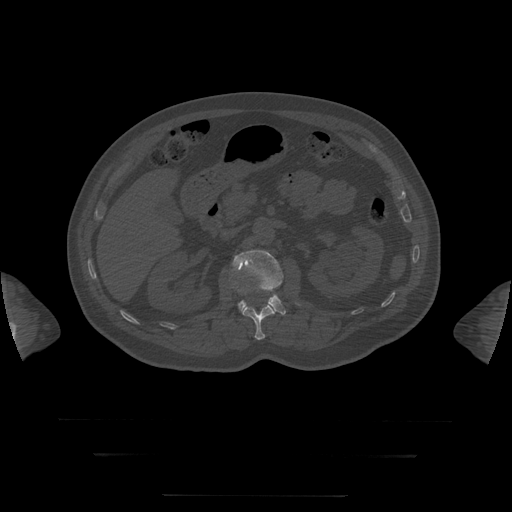
CT including the spine, one axial slice. Position 36 of 397 along the scan axis. 120 kVp. Bone window (W 1800 / L 400 HU). 1.25 mm slice thickness. 512 × 512 image matrix, field of view 510 × 510 mm. Patient age 73 years. From the clinical record (not read from this slice): primary cancer: prostate.
Outlined on this slice (semi-automatic segmentation, software-assisted and operator-edited):
- L1 vertebra: box from (x=232, y=287) to (x=275, y=340) px